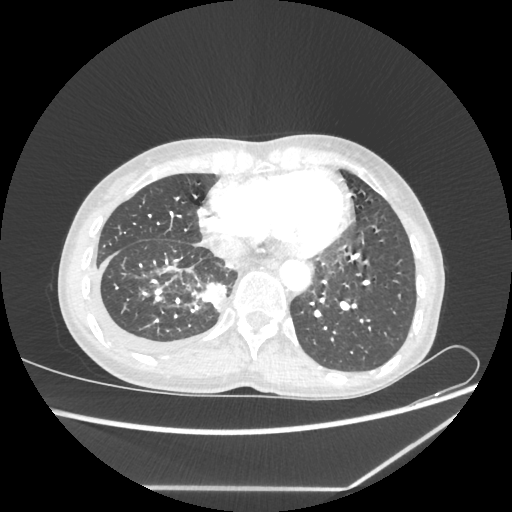
Chest CT, one axial slice. Position 70 of 237 along the scan axis. Reconstruction kernel STANDARD. Lung window (W 1500 / L -600 HU). 1.25 mm slice thickness. 512 × 512 image matrix. Female patient, age 59 years. From the clinical record (not read from this slice): clinical TNM (as recorded): T1c N1 M1.
Structures marked on this image (rectangle marked by the reading radiologist):
- lung tumour (recorded histology: adenocarcinoma): bounding box [x1, y1, x2, y2] px = [201, 279, 227, 315]